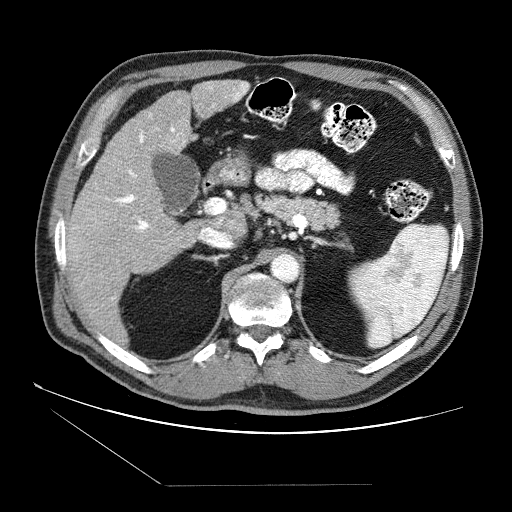
Contrast-enhanced abdominal CT (liver protocol), one axial slice. Slice 43 of 87 in the series (ordered by position). Reconstruction kernel STANDARD. Soft-tissue window (W 400 / L 40 HU). 2.5 mm slice thickness. 512 × 512 image matrix, field of view 400 × 400 mm. Case-level facts recorded for this patient, not image findings: diagnosis: hepatocellular carcinoma (patient treated with transarterial chemoembolisation; whether this scan precedes or follows treatment is not stated here); TNM stage (as recorded): Stage-II; Child-Pugh class: B; tumour differentiation: no biopsy; tumour size: 2.6 cm.
Outlined on this slice (semi-automatically segmented with operator editing):
- liver parenchyma outside the tumour (the mass and vessels are separate outlines, so this box may not span the whole liver): bounding box <64,80,248,336> (left, top, right, bottom; pixels)
- liver vessels: <70,82,248,300>